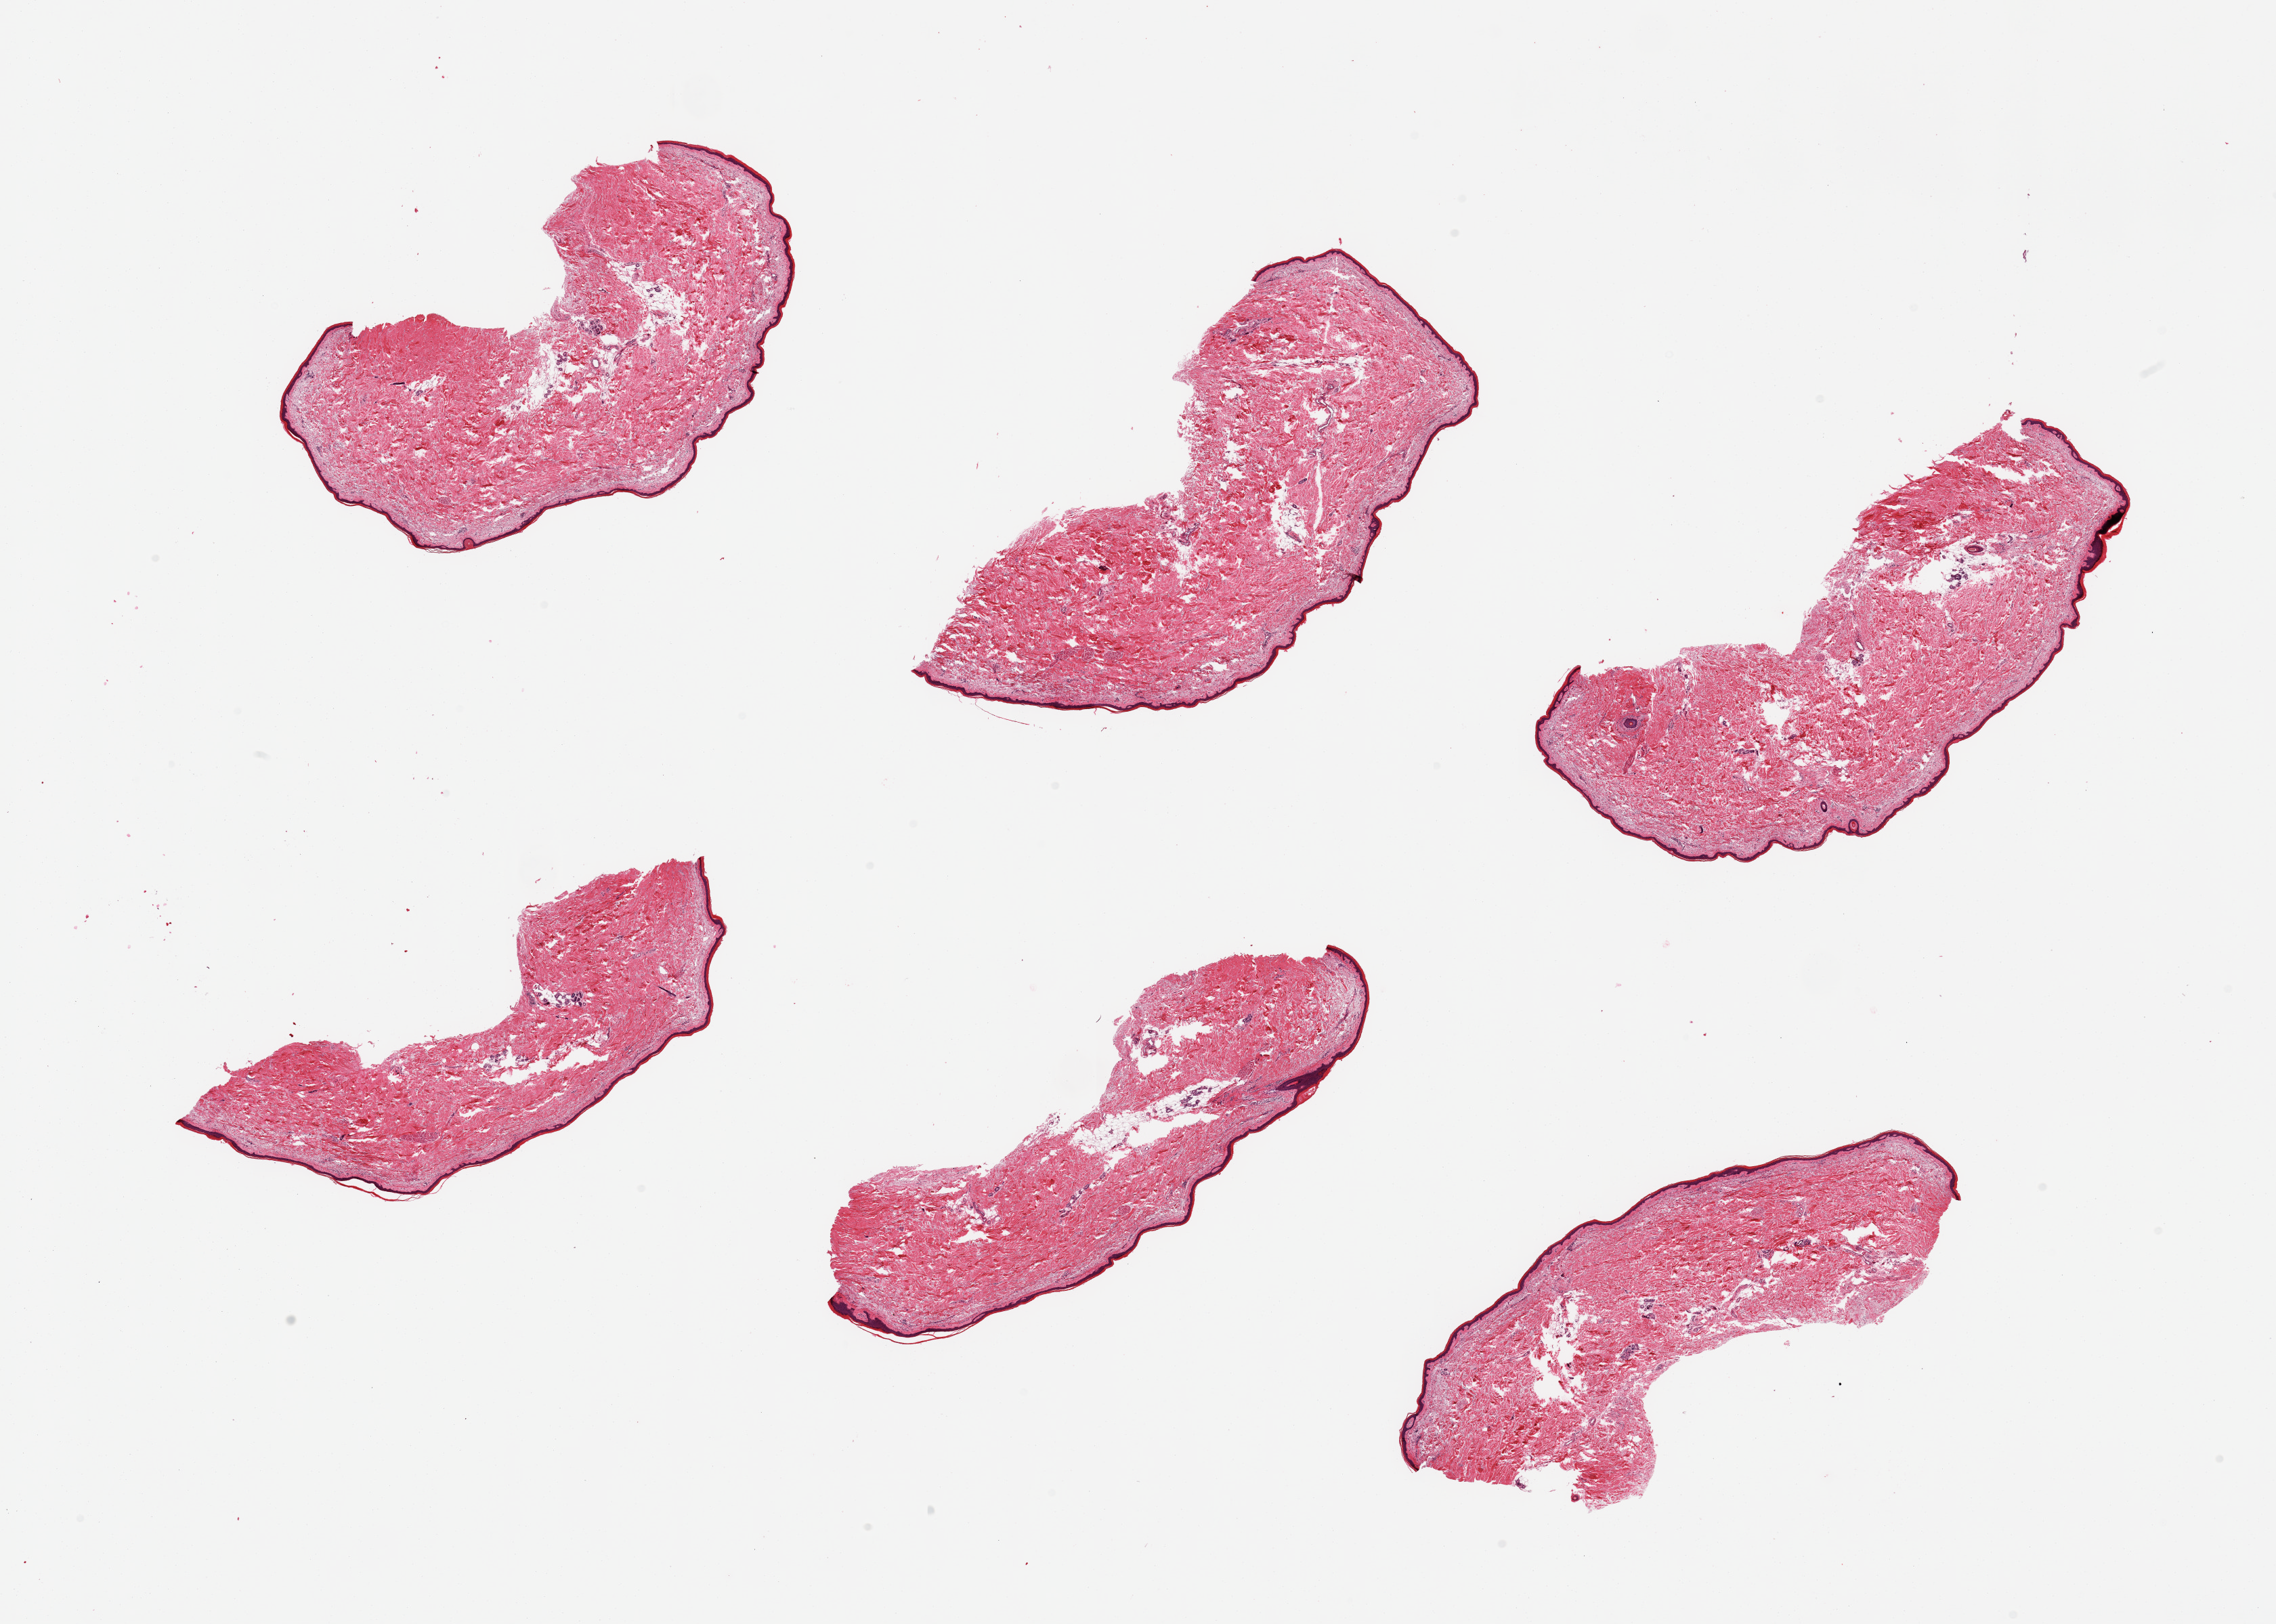
Haematoxylin and eosin whole-slide image — whole scanned area (about 26.6 x 19.0 mm, from a 20x scan) shown as a low-resolution overview; PAXgene-fixed, paraffin-embedded tissue; section of skin of lower leg (target tissue); donor tissue sample.
* reviewer comment on this tissue sample: 6 pieces; well trimmed with ~10% internal fat; solar elastosis